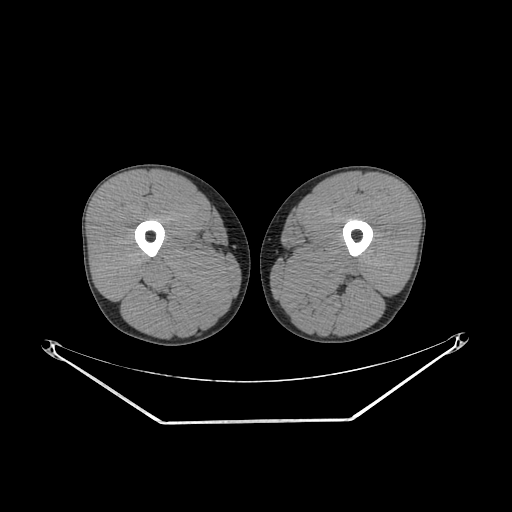
CT of an extremity soft-tissue mass (from a PET/CT study), one axial slice. Position 225 of 267 along the scan axis. 140 kVp. Soft-tissue window (W 400 / L 40 HU). 512 × 512 image matrix. Male patient. Case-level facts recorded for this patient, not image findings: histological type: extraskeletal osteosarcoma; grade: high; site of the primary tumour: left adductur.
Annotated regions visible in this slice (expert contour drawn on MRI and transferred to this co-registered scan by the dataset authors):
- gross tumour volume (mass): box from (x=281, y=246) to (x=369, y=305) px